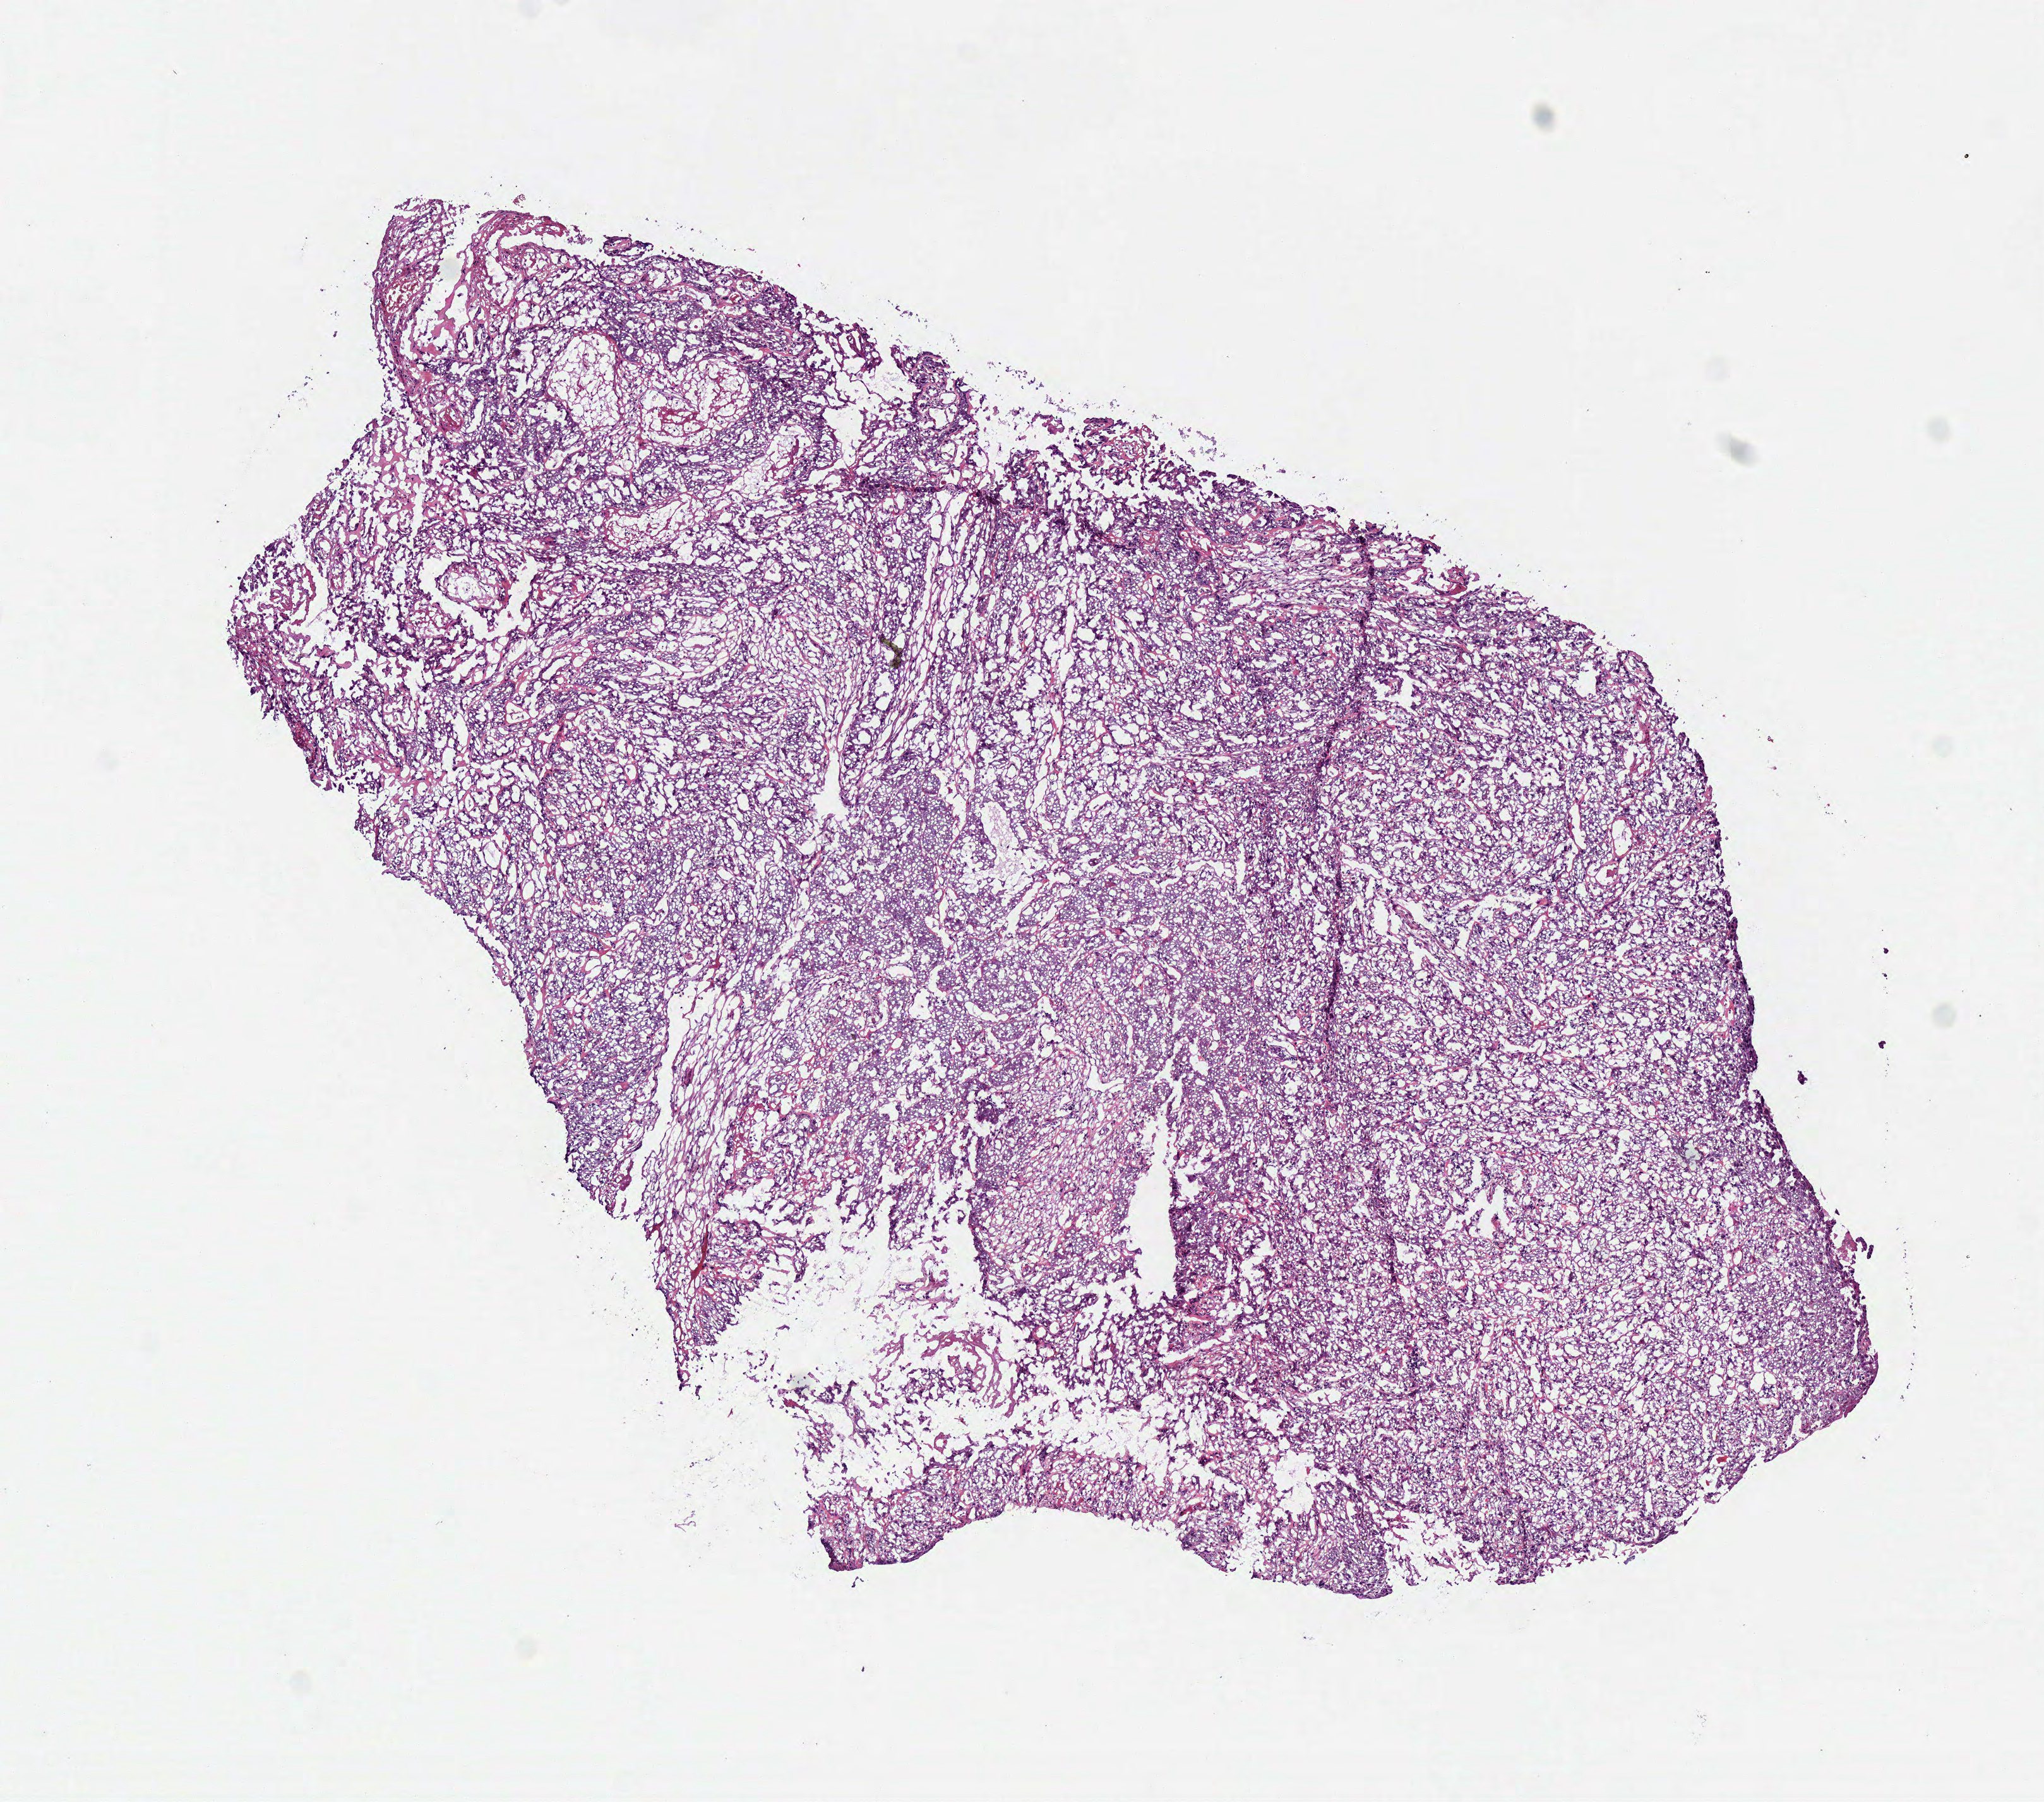
Digitized H&E-stained tissue section (whole slide) — low-resolution overview of the scanned area, about 6.4 x 5.6 mm; frozen section; primary tumour sample from the head and neck. Patient: male, age at initial diagnosis 52 years. Histologic grade: G3 (poorly differentiated). Pathologist review of this section (percent, as recorded): tumour cells 95%, tumour nuclei 85%, normal cells 0%, stromal cells 5%, necrosis 0%.
Diagnosis: Squamous cell carcinoma, NOS. Laterality: left.